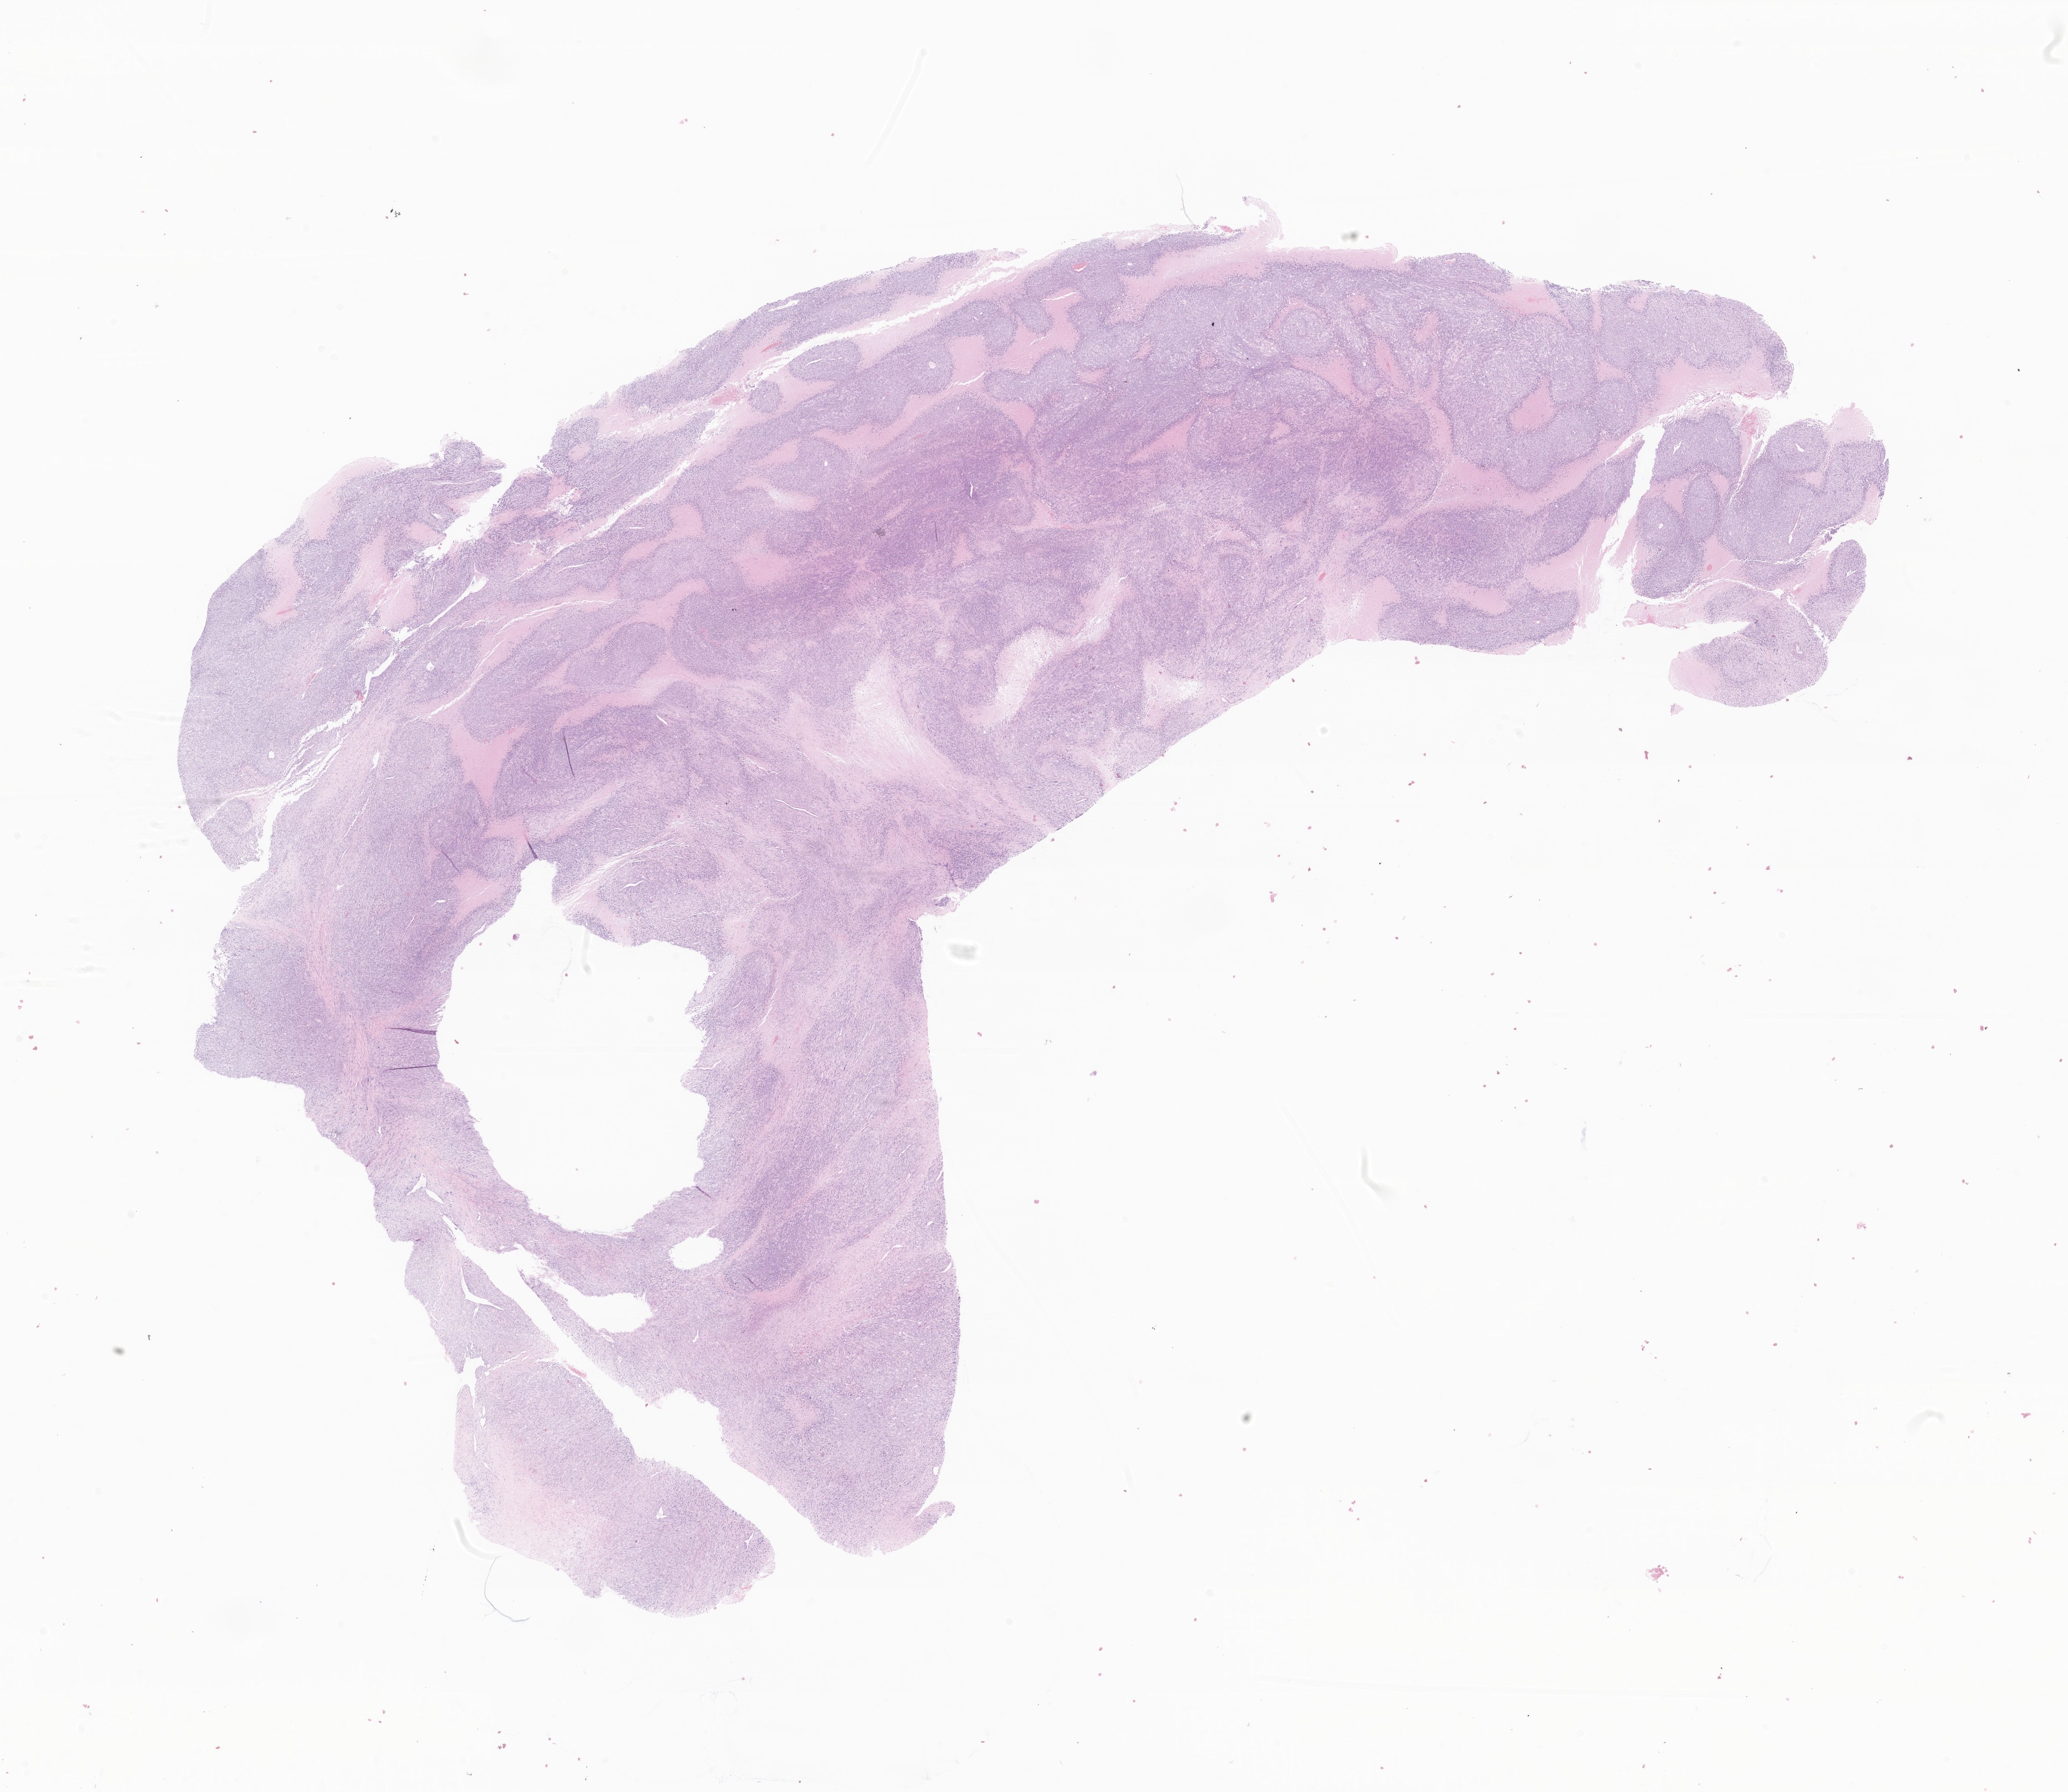
Haematoxylin and eosin whole-slide image of tumor tissue from the abdomen, shown as a low-resolution overview of the whole scanned area (about 21.4 x 18.6 mm); formalin-fixed, paraffin-embedded (FFPE) tissue. Male patient, age 55 months (4 years 7 months).
• diagnosis (ICD-O-3 morphology term): Embryonal rhabdomyosarcoma, NOS